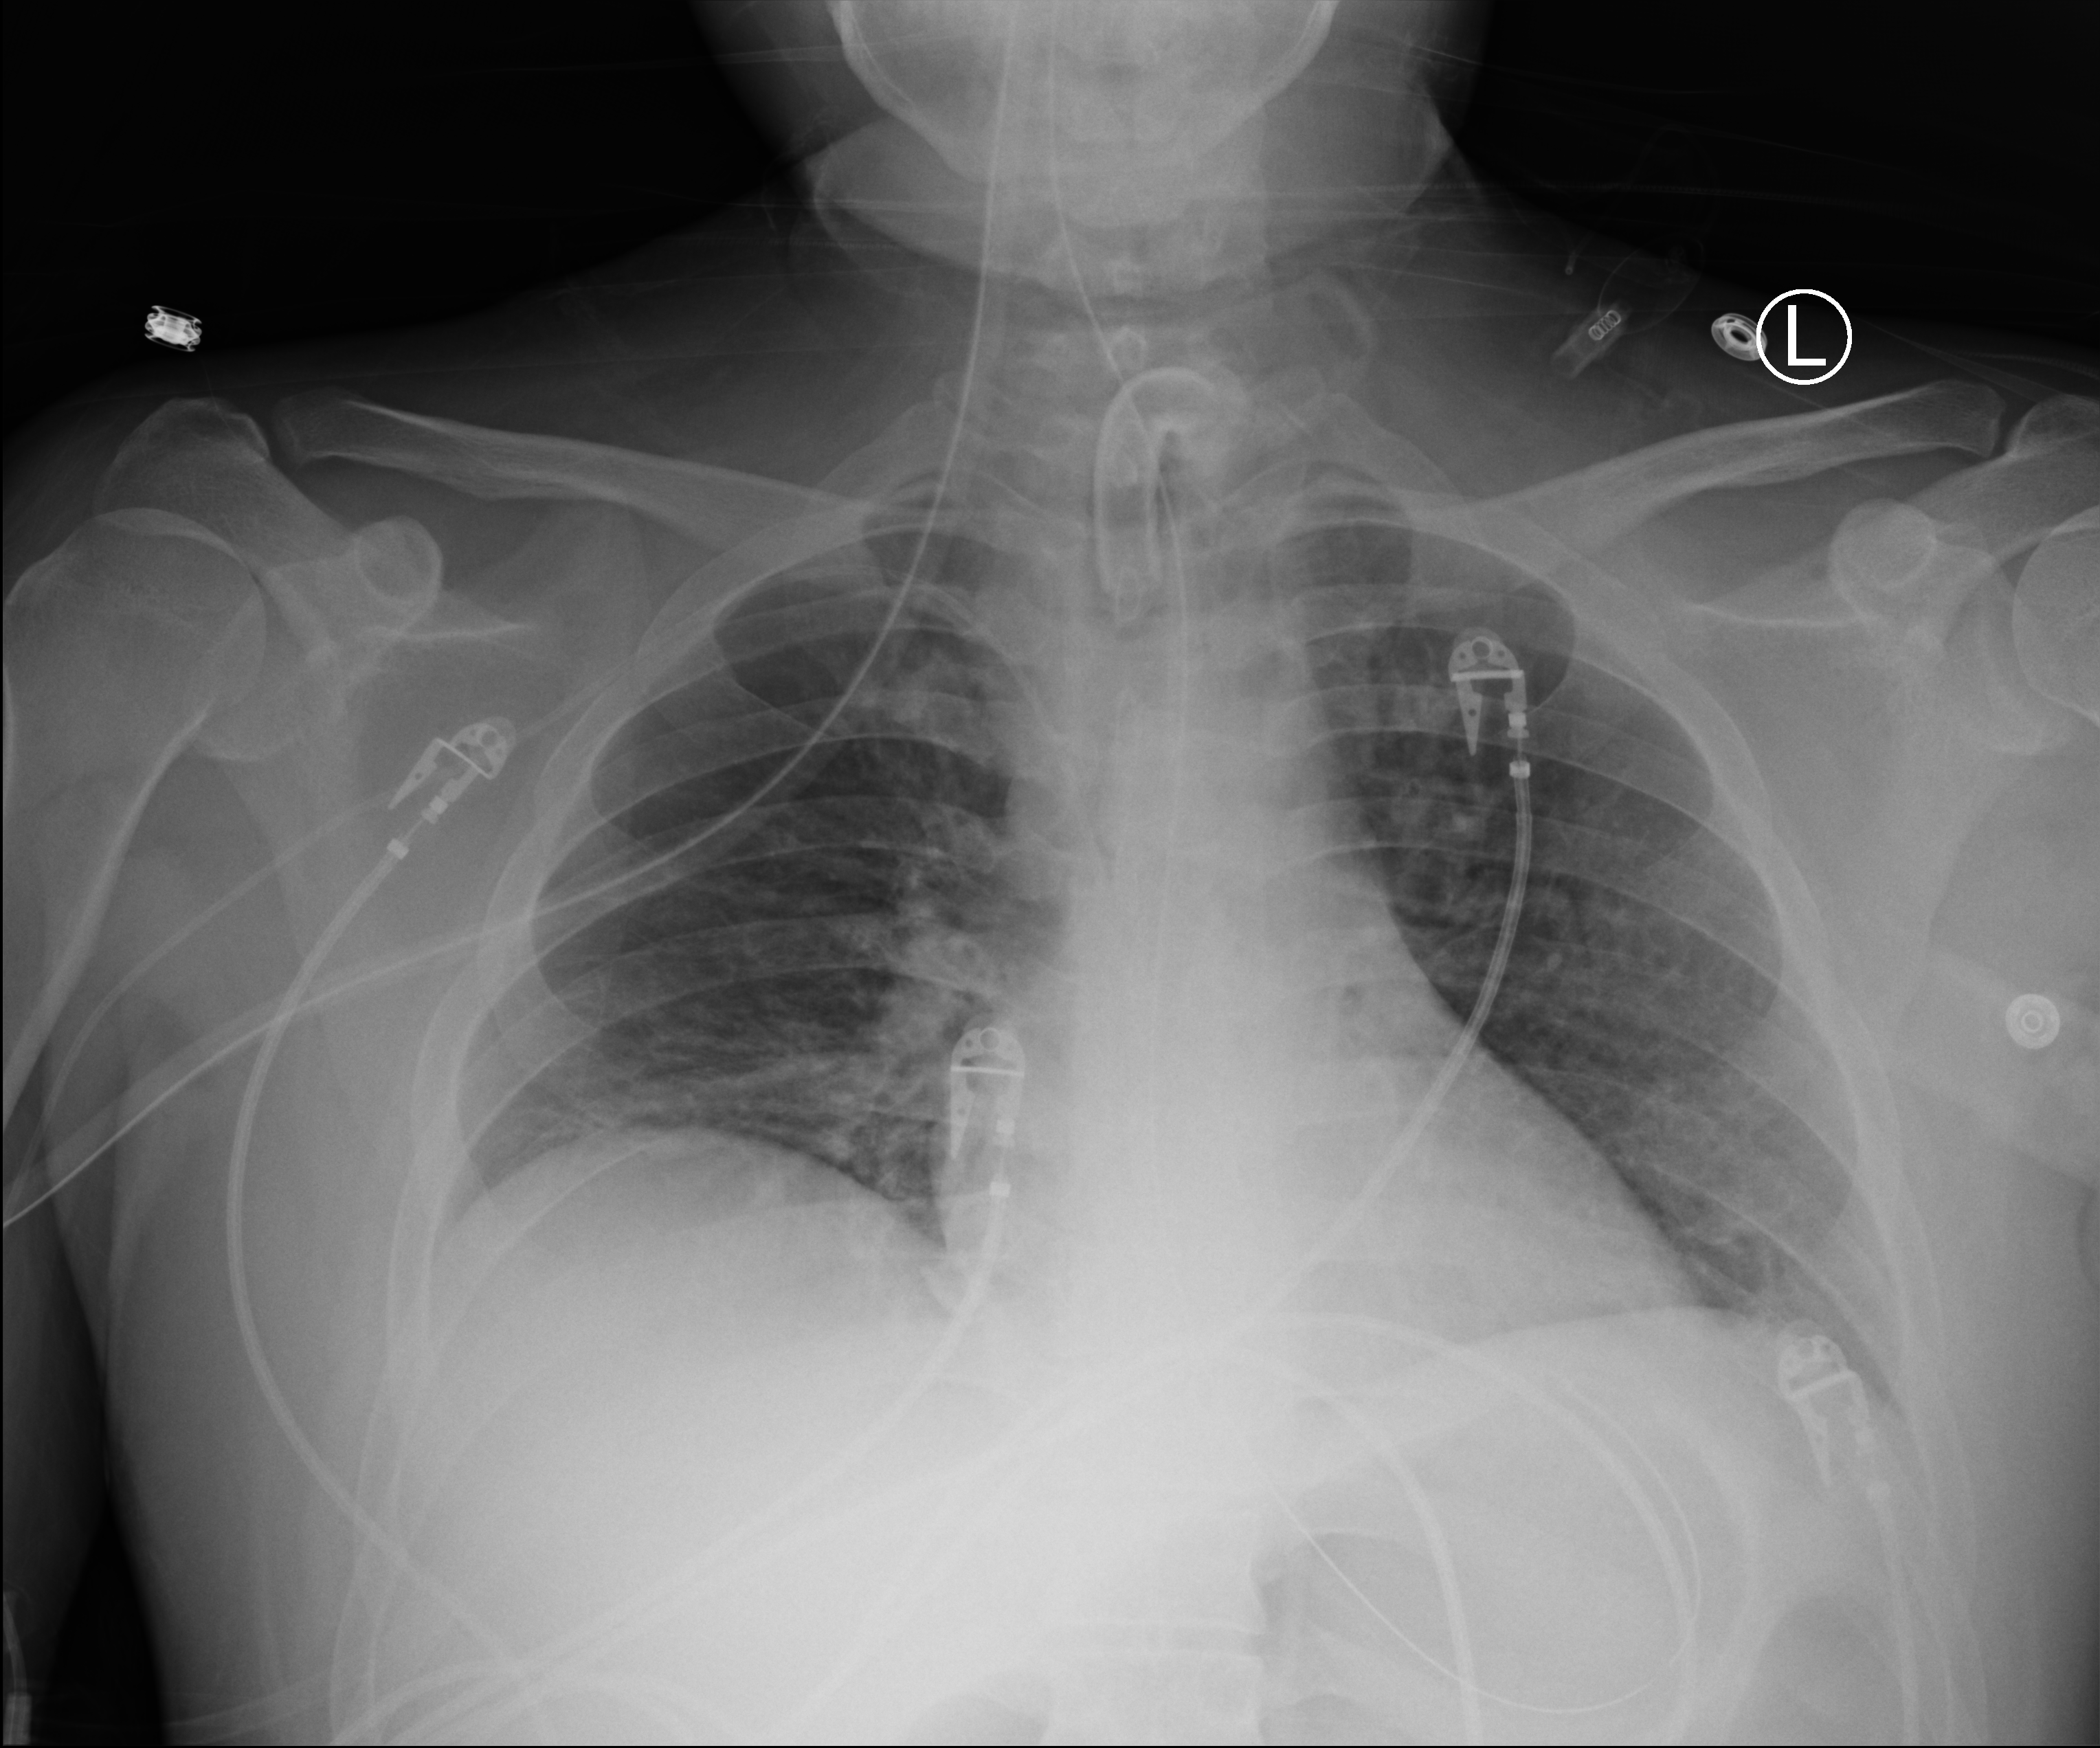
Bedside chest radiograph (computed radiography); anteroposterior (AP) projection. Patient hospitalised with COVID-19; male, aged 18–59 years.
Admission-level facts for this patient (not findings on this image; timing relative to this image not recorded):
- COPD (admission record): no
- other chronic lung disease (admission record): no
- mechanically ventilated during this hospital stay: yes